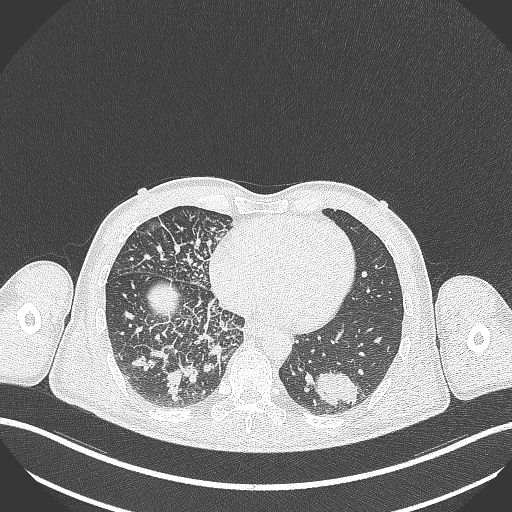
Chest CT, one axial slice. Slice 103 of 348 in the series (ordered by position). 120 kVp. Lung window (W 1500 / L -600 HU). 1 mm slice thickness. 512 × 512 image matrix, field of view 400 × 400 mm. Male patient, age 49 years. From the clinical record (not read from this slice): clinical TNM (as recorded): T2b N1 M0.
Outlined on this slice (rectangle marked by the reading radiologist):
- lung tumour (recorded histology: adenocarcinoma): box from (x=313, y=364) to (x=361, y=407) px